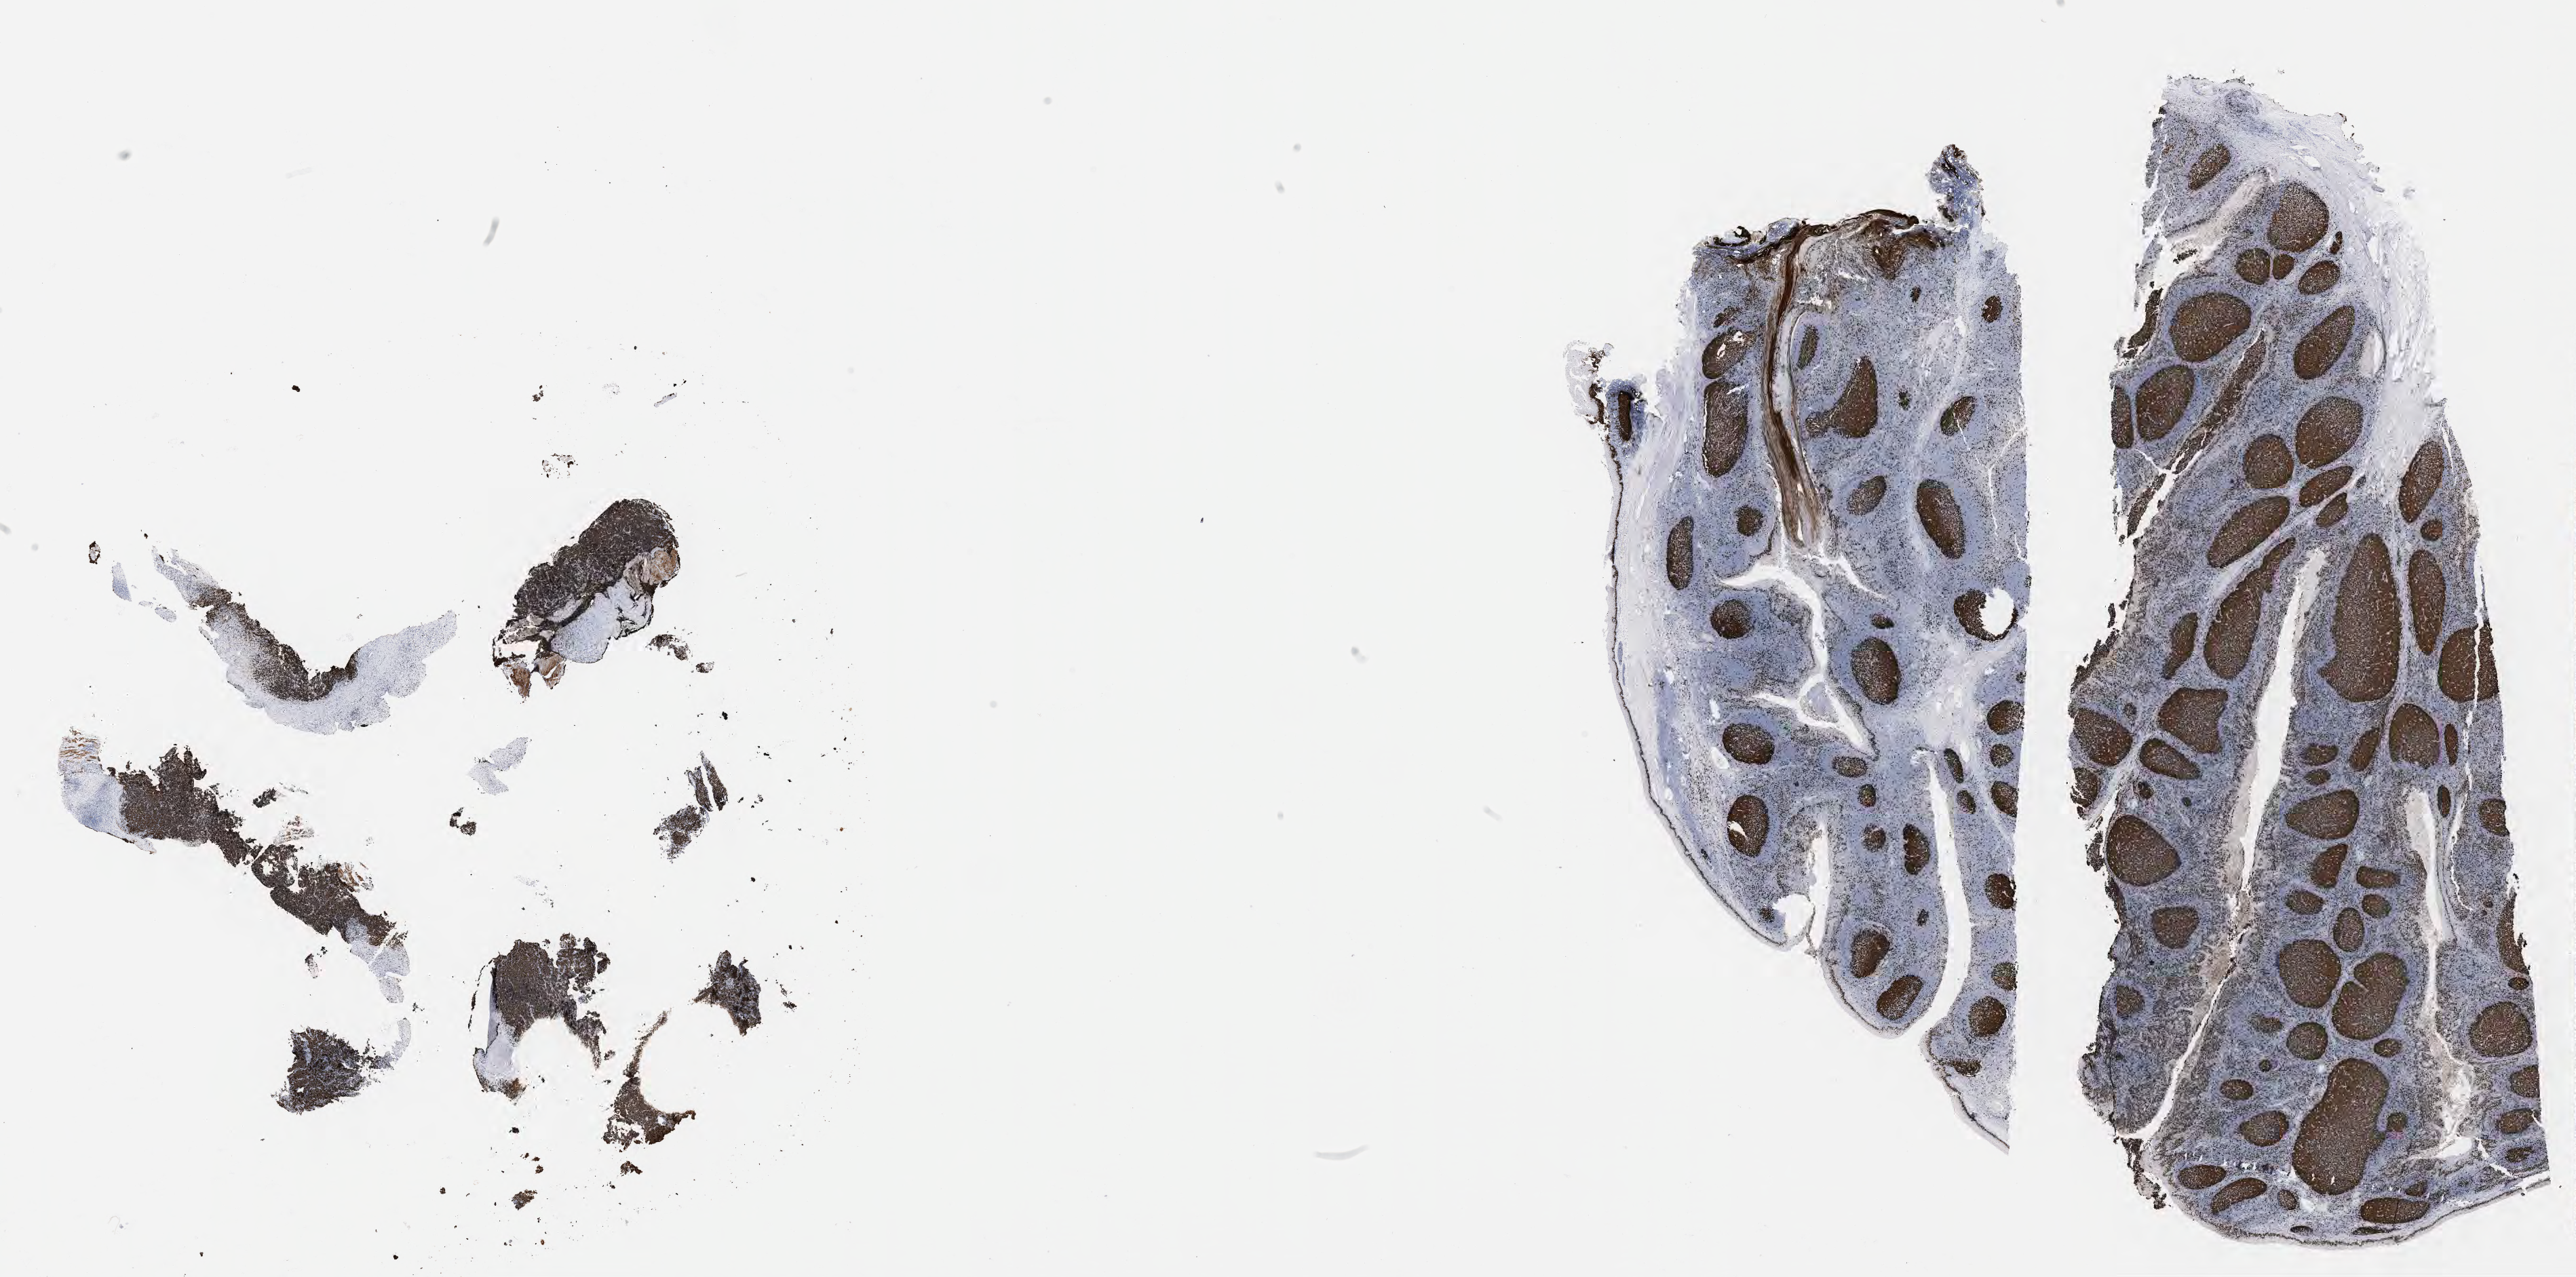
Whole-slide image, immunohistochemical stain for Ki-67, low-resolution overview of the scanned area, about 30.7 x 15.2 mm. Tumor tissue. Female patient; age at initial diagnosis 9 years.
- diagnosis: Burkitt lymphoma, NOS